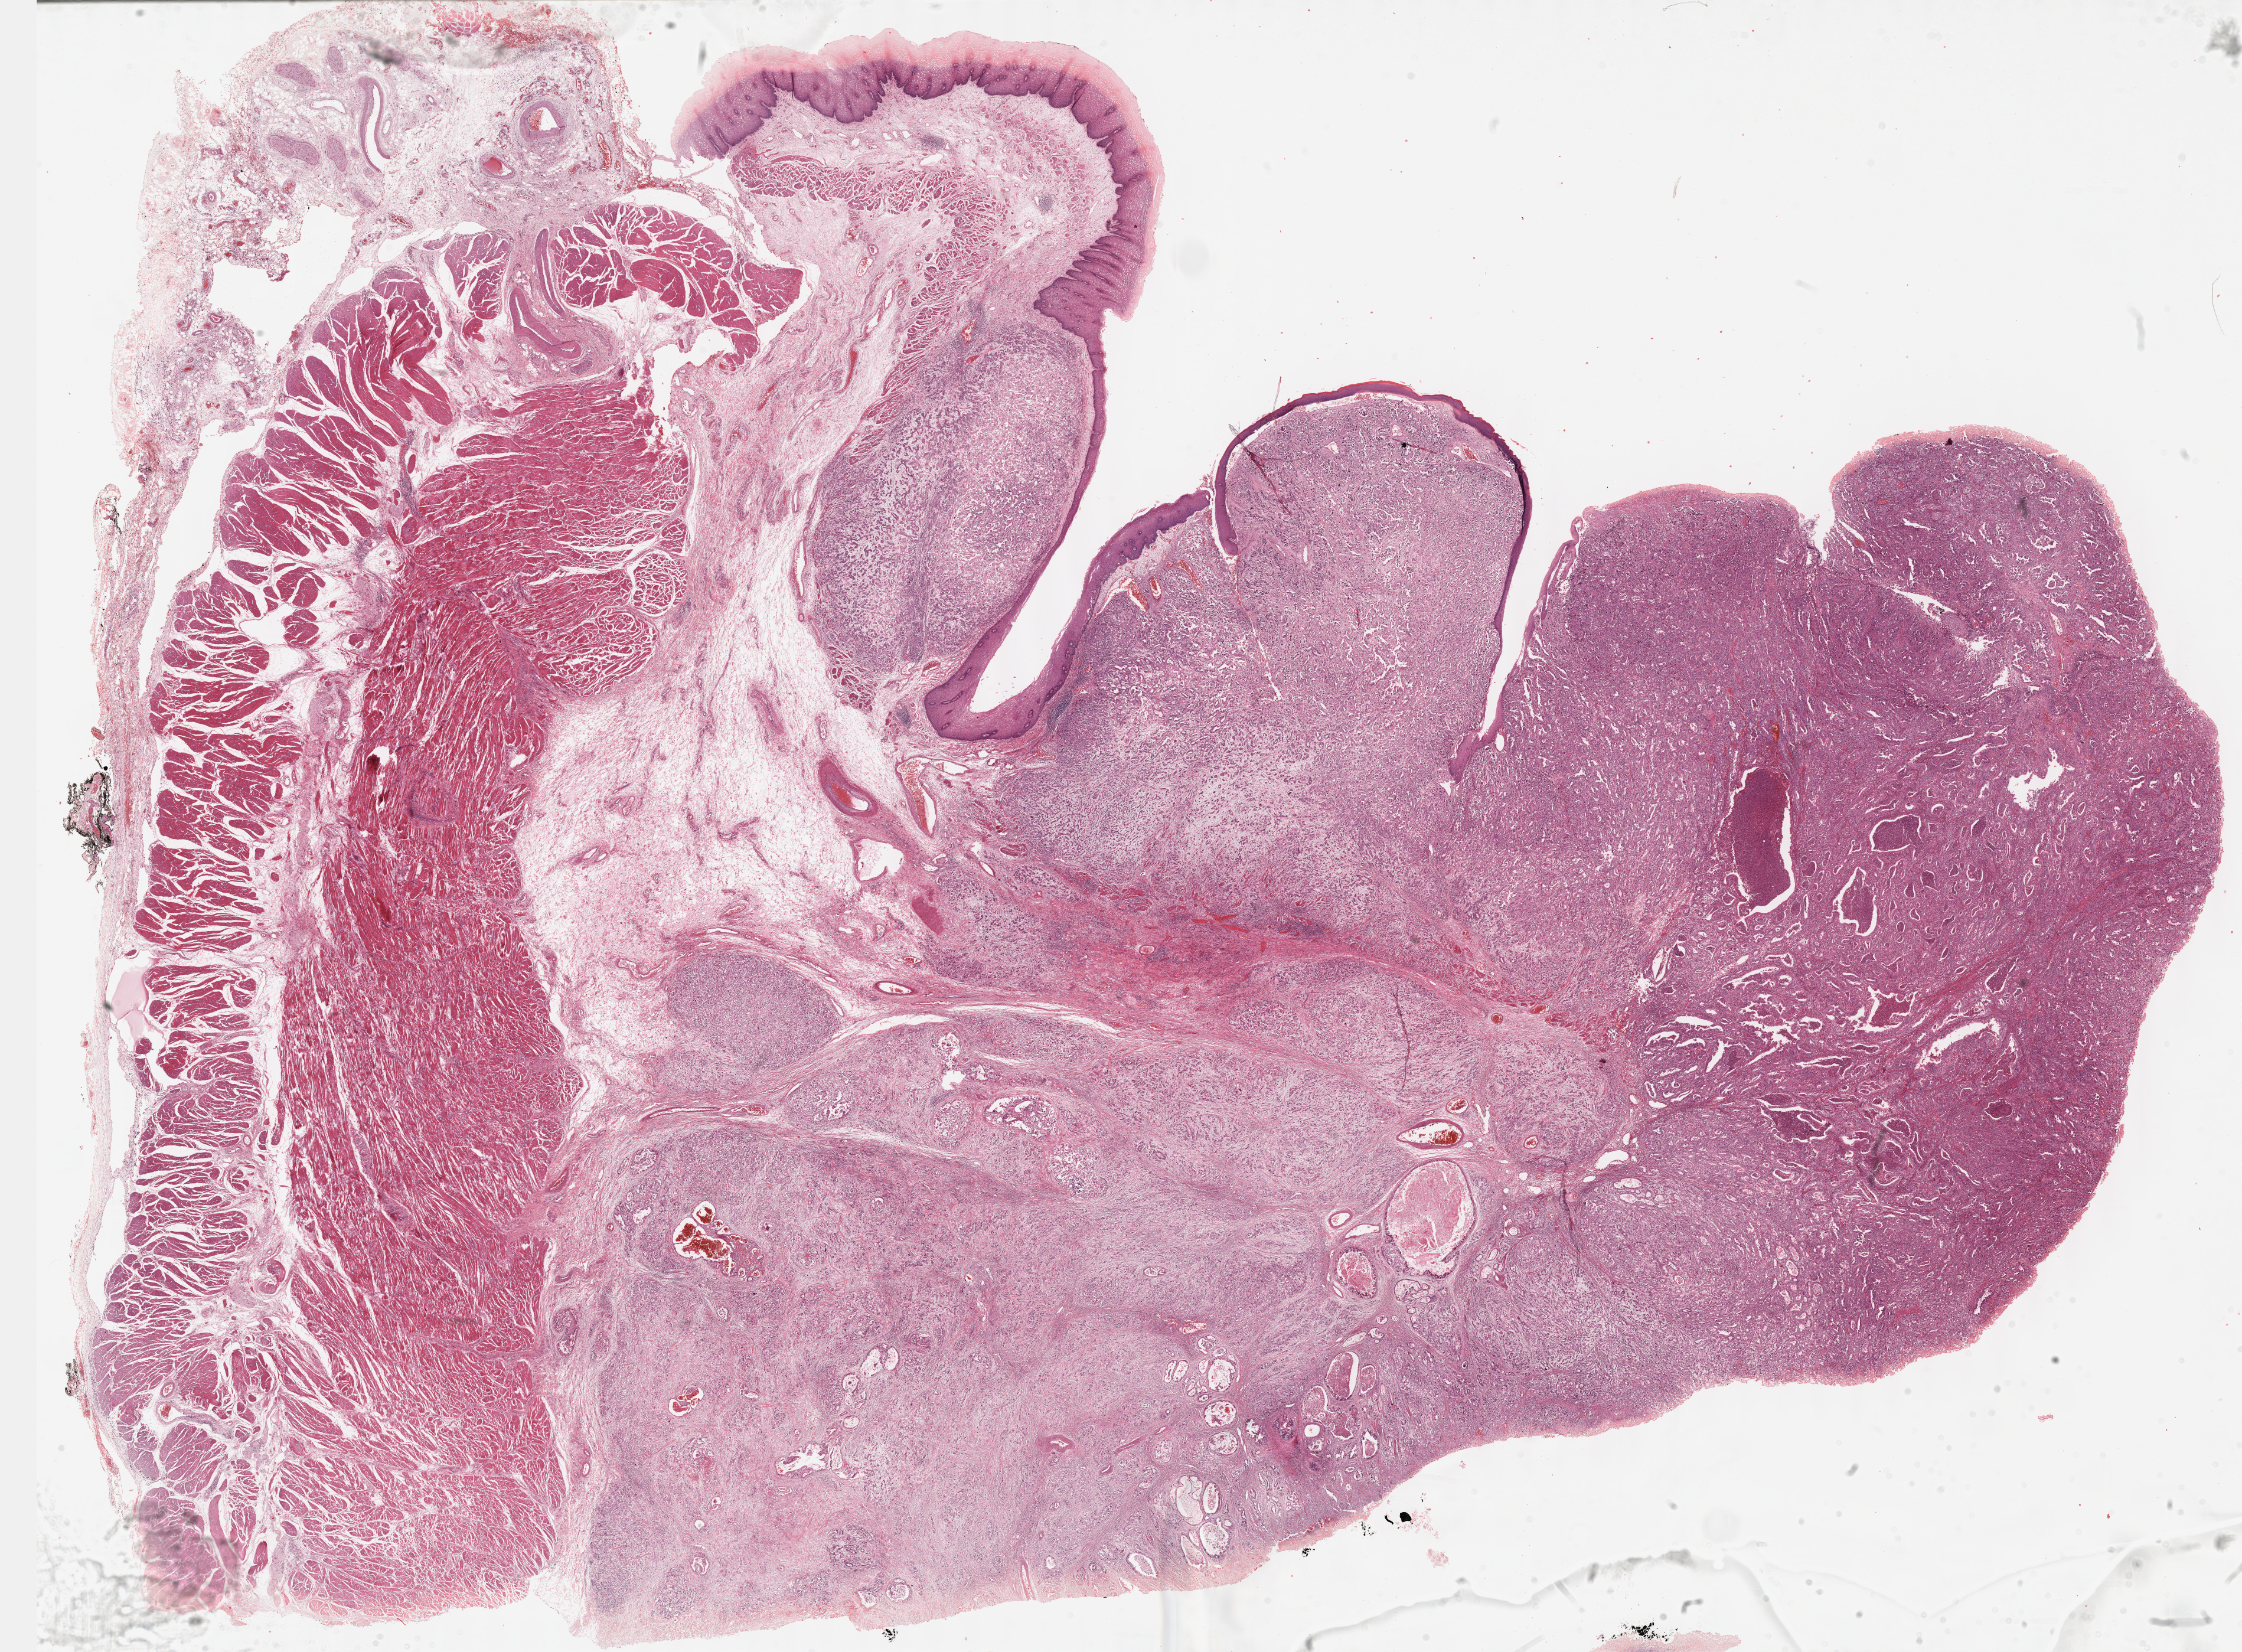
Digitized Hematoxylin and eosin (H&E) stained tissue section (whole slide), a low-resolution overview of the entire scanned area, about 30.7 x 22.6 mm (from a 40x scan); formalin-fixed paraffin-embedded (FFPE) diagnostic section; primary tumour sample from the esophagus. Male patient; age at initial diagnosis 58 years. Histologic grade: G3 (poorly differentiated).
- AJCC pathologic stage: IVA (5th edition)
- histologic diagnosis: Adenocarcinoma, NOS (lower third of esophagus)
- lymph nodes positive (case pathology): 9 of 13 examined